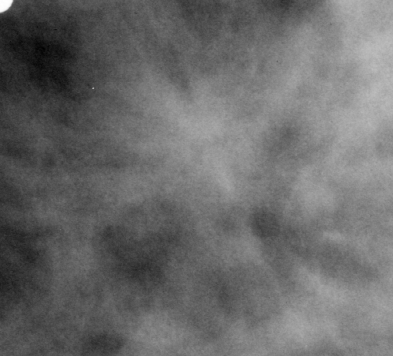
Crop from a digitized film mammogram around one marked abnormality; left breast; MLO view.
Mass, shape architectural distortion, margins ill defined; BI-RADS assessment category 4; subtlety rating 3 on a 1 (subtle) to 5 (obvious) scale; pathology (as recorded): malignant.